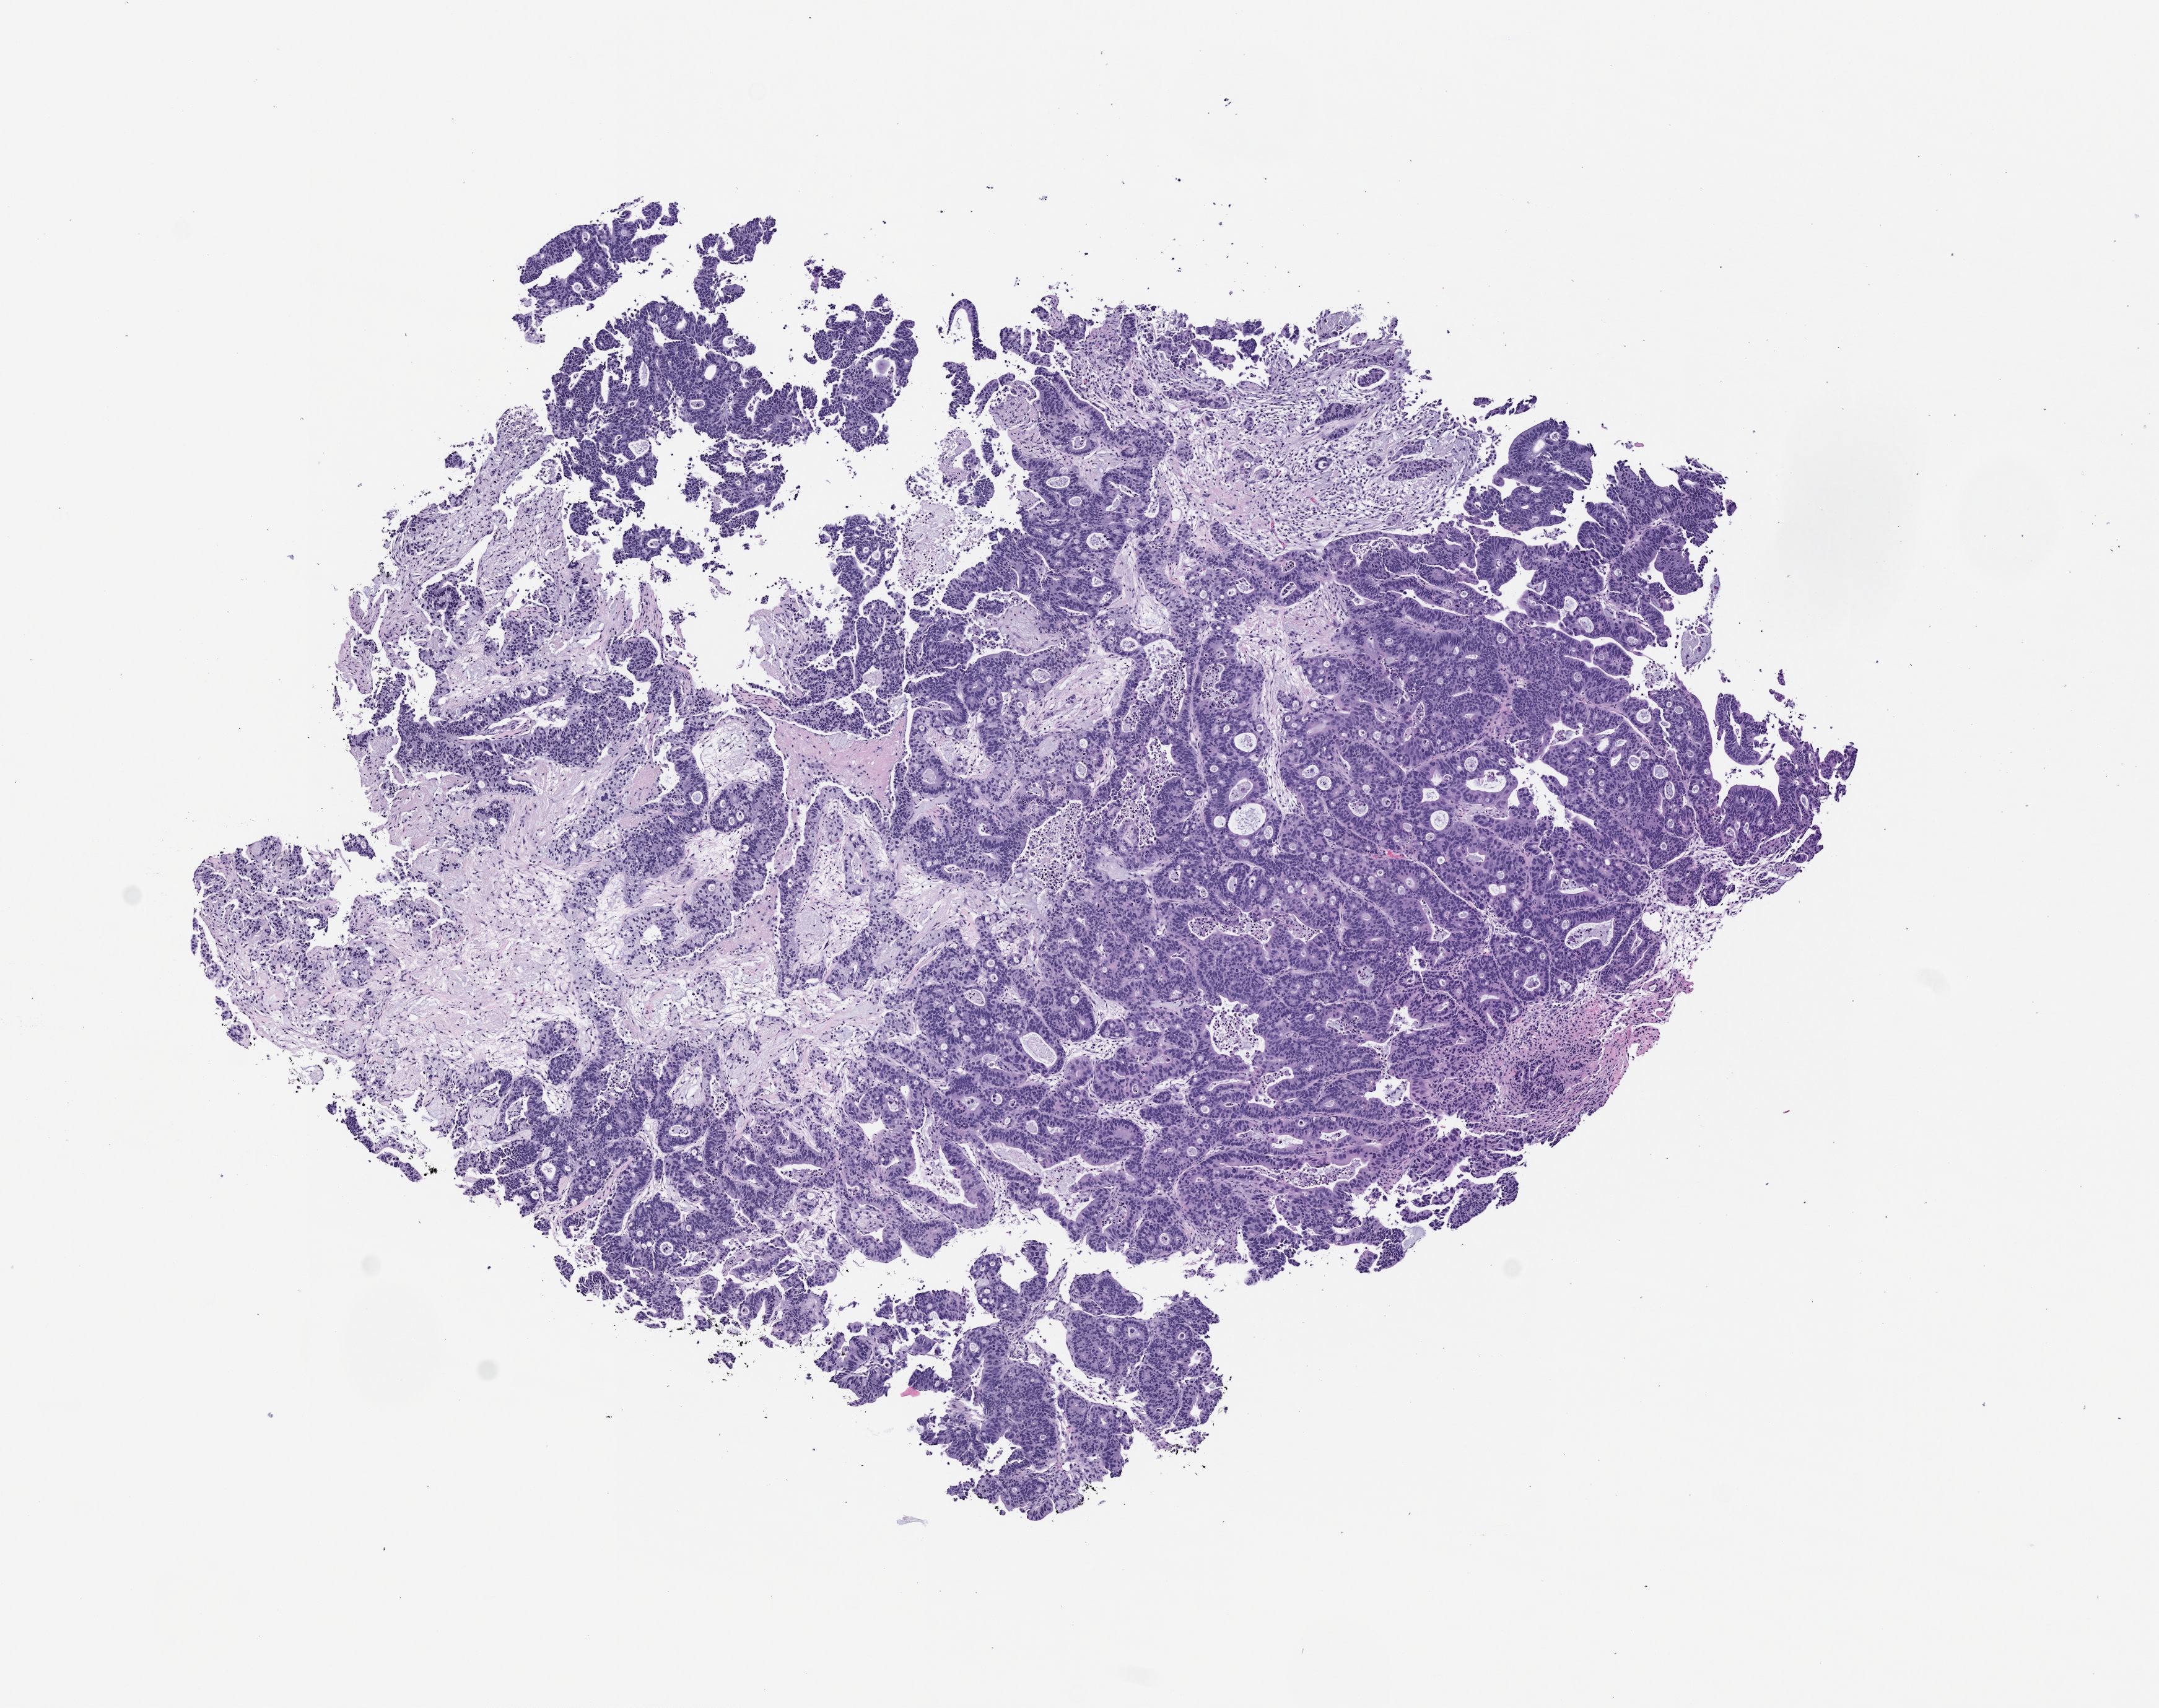
Whole-slide image, hematoxylin and eosin (H&E): patient-derived xenograft (human tumor grown in a mouse), passage 1, whole scanned area (about 7.0 x 5.5 mm) shown as a low-resolution overview; FFPE section; originating tumor site category: rectum.
• originating patient diagnosis: Rectal Adenocarcinoma